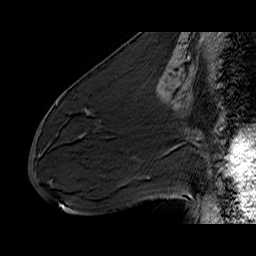
Breast MRI (dynamic contrast-enhanced), one sagittal slice. Dynamic contrast-enhanced series, time point 2 of 6 at this slice position (early post-contrast). 1.5 T. TE 6.5 ms, TR 32.9 ms. 4 mm slice thickness. 256 × 256 image matrix, field of view 200 × 200 mm. Female patient. From the clinical record (not read from this slice): setting: breast cancer imaged before/during neoadjuvant chemotherapy; receptor status: HER2-positive.
Outlined on this slice (semi-automatically segmented with operator editing):
- analysis volume of interest (the breast-tissue region the enhancement analysis was run in; not a lesion): bounding box <72,88,133,137> (left, top, right, bottom; pixels)
- tumour enhancement mask (voxels above the 100 % enhancement threshold inside the analysis volume of interest): <87,112,90,115>